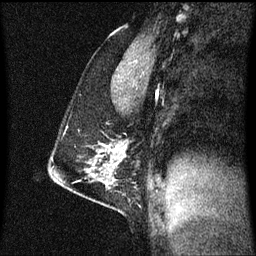
Breast MRI (dynamic contrast-enhanced), one sagittal slice. Position 37 of 60 along the scan axis. Dynamic contrast-enhanced series, image 2 of 3 at this slice position (ordered by acquisition). 1.5 T. TE 4.2 ms, TR 8.4 ms. 256 × 256 image matrix, field of view 200 × 200 mm. Patient: female, 40 years. From the clinical record (not read from this slice): setting: breast cancer imaged before/during neoadjuvant chemotherapy; receptor status: triple-negative.
Outlined on this slice (semi-automatically segmented with operator editing):
- analysis volume of interest (the breast-tissue region the enhancement analysis was run in; not a lesion): bounding box <50,140,131,195> (left, top, right, bottom; pixels)
- tumour enhancement mask (voxels above the 70 % enhancement threshold inside the analysis volume of interest): <117,146,125,147>